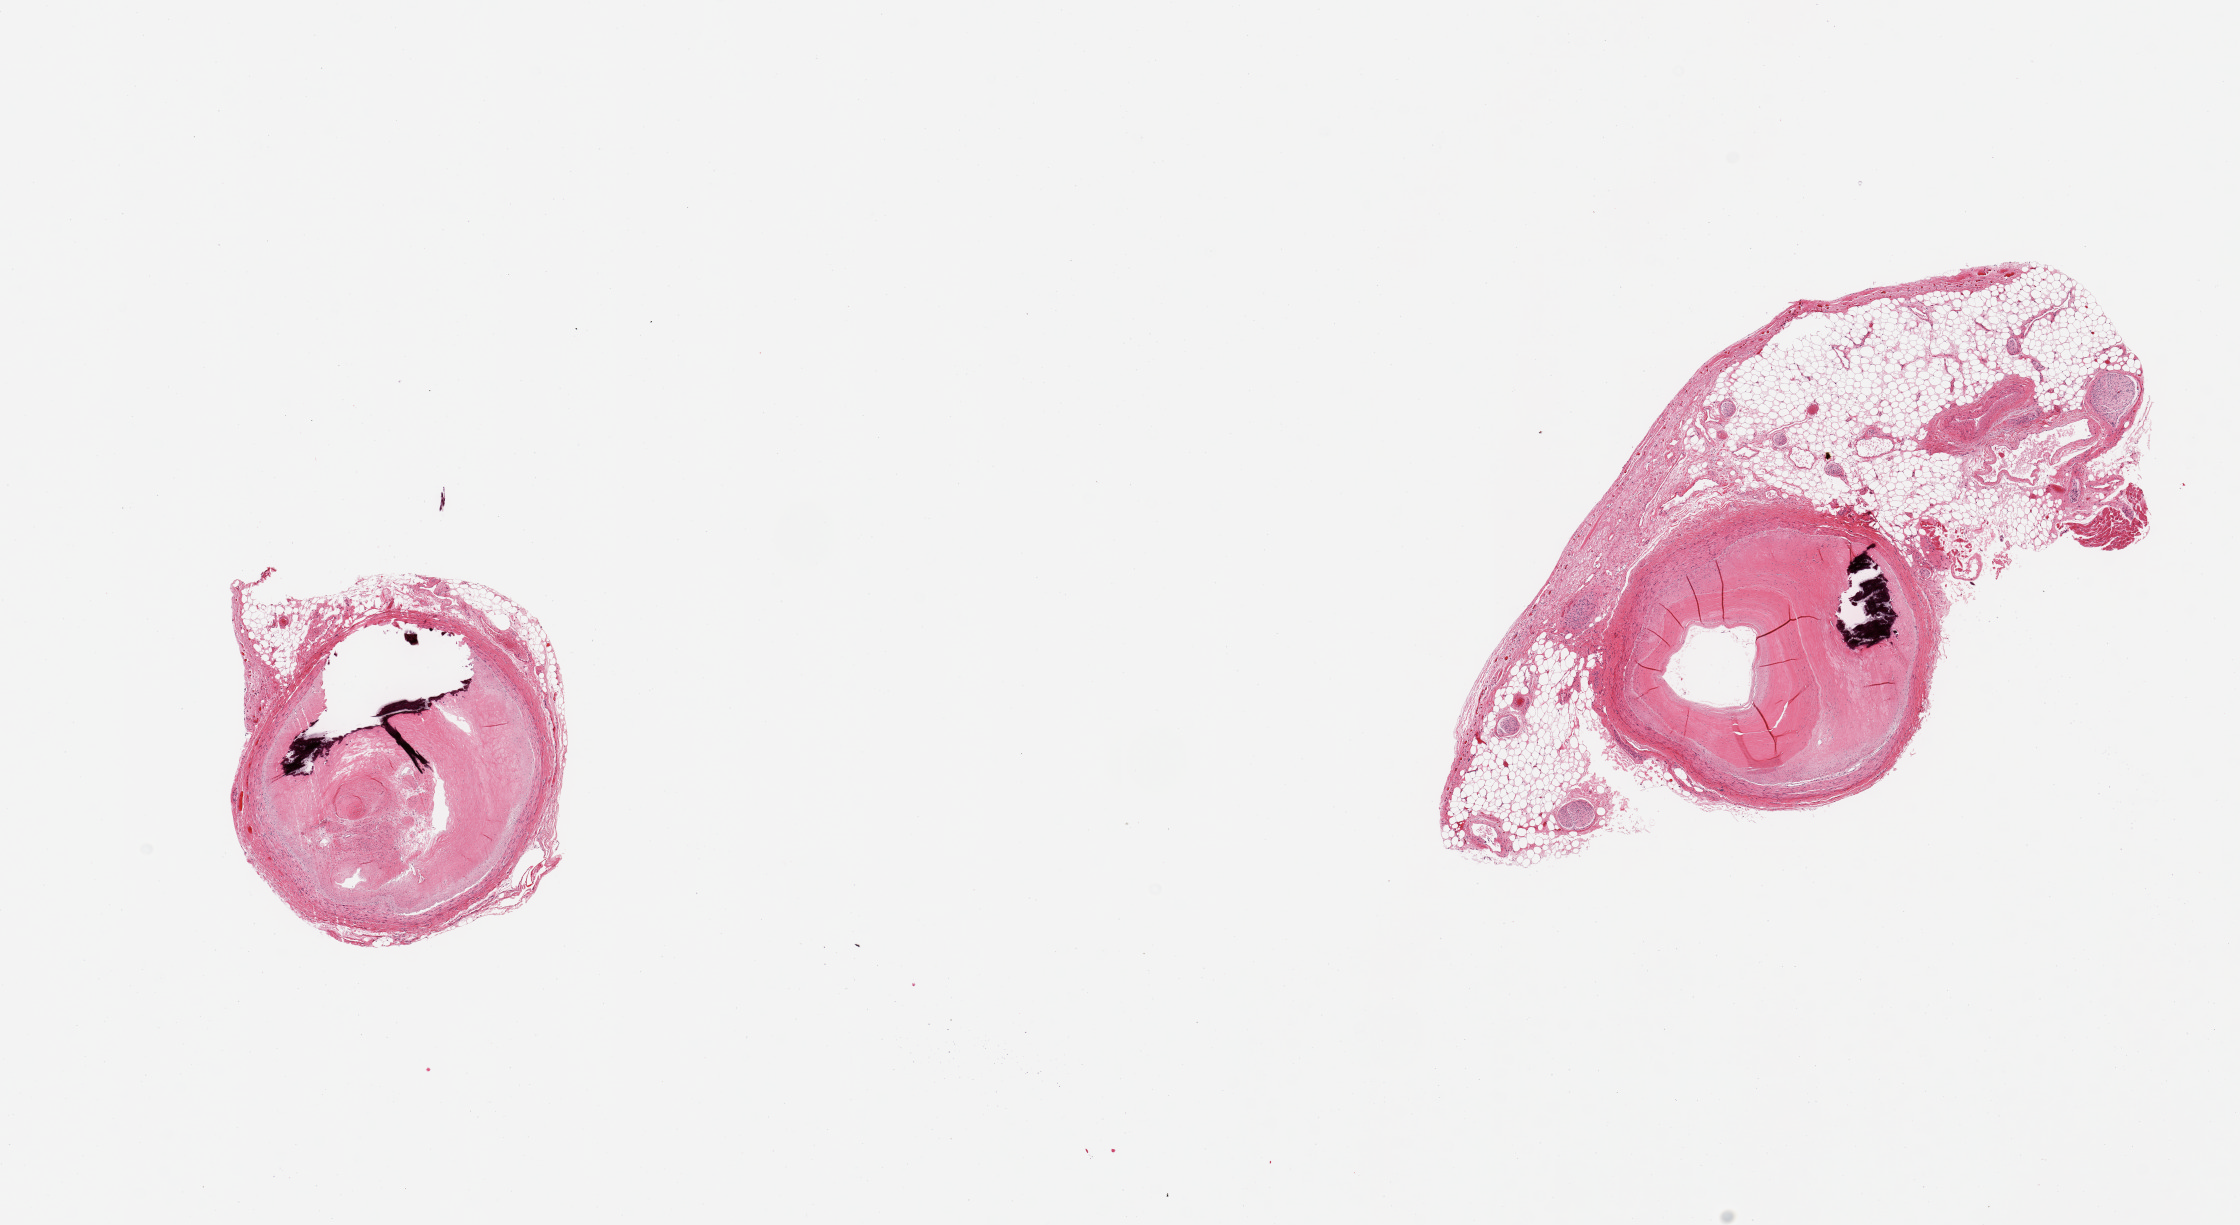
Whole-slide image, hematoxylin and eosin (H&E) stain — whole scanned area (about 17.7 x 9.7 mm, slide scanned at 20x) shown as a low-resolution overview, PAXgene-fixed, paraffin-embedded tissue, sampled site (target tissue): coronary artery, tissue donor sample. Donor: female.
Review note (as recorded): 2 pieces; extensive occlusive calcified atheromatous plaques narrowing lumen by 80% in 1 and possibly totally occluded in other; 1 piece with 50% external fat; sample is of limited value due to small amount of normal tissue remaining.